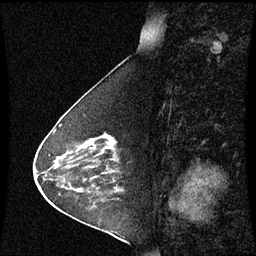
Breast MRI (dynamic contrast-enhanced), one sagittal slice; position 26 of 60 along the scan axis; dynamic contrast-enhanced series, image 2 of 3 at this slice position (ordered by acquisition); 1.5 T; TE 4.2 ms, TR 8.9 ms; 256 × 256 image matrix, field of view 210 × 210 mm. Female patient, age 63 years. From the clinical record (not read from this slice): setting: breast cancer imaged before/during neoadjuvant chemotherapy; receptor status: HR-positive, HER2-negative.
Outlined on this slice (semi-automatic segmentation, software-assisted and operator-edited):
- analysis volume of interest (the breast-tissue region the enhancement analysis was run in; not a lesion): bounding box <76,135,122,178> (left, top, right, bottom; pixels)
- tumour enhancement mask (voxels above the 70 % enhancement threshold inside the analysis volume of interest): <105,135,116,144>